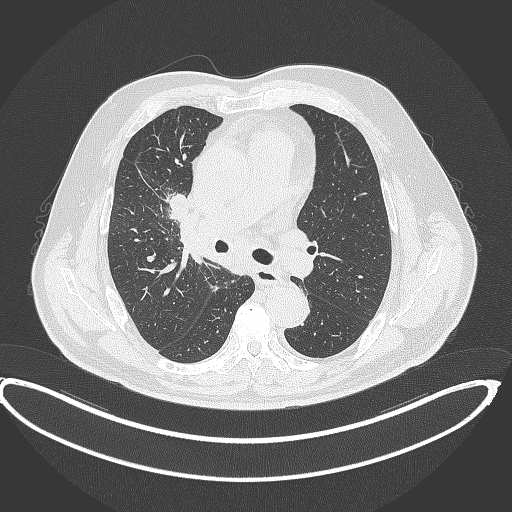
Chest CT, one axial slice; lung window (W 1500 / L -600 HU); 512 × 512 image matrix. Patient: male, 62 years. From the clinical record (not read from this slice): clinical TNM (as recorded): T1c N3 M1c.
Annotated regions visible in this slice (rectangle marked by the reading radiologist):
- lung tumour (recorded histology: adenocarcinoma): box from (x=164, y=191) to (x=188, y=221) px